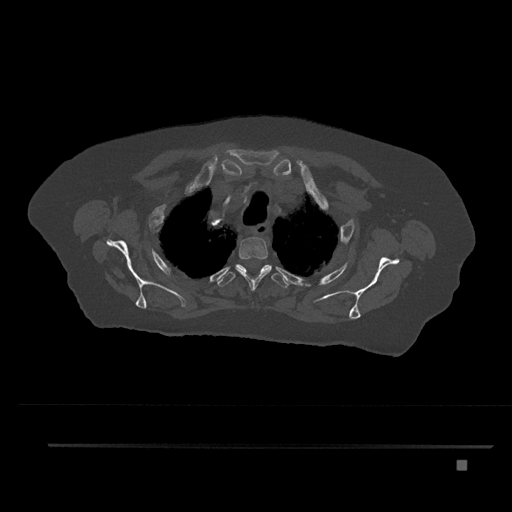
CT including the spine, one axial slice; slice 655 of 797 in the series (ordered by position); reconstruction kernel Br40s/3; 120 kVp; bone window (W 1800 / L 400 HU); 0.5 mm slice thickness; 512 × 512 image matrix. Female patient, age 76 years. From the clinical record (not read from this slice): primary cancer: lung; vertebrae with lytic lesions (as recorded): T11, L3.
Structures marked on this image (semi-automatic segmentation, software-assisted and operator-edited):
- T2 vertebra: box from (x=235, y=231) to (x=272, y=291) px
- T3 vertebra: (x=218, y=264)–(x=288, y=288)